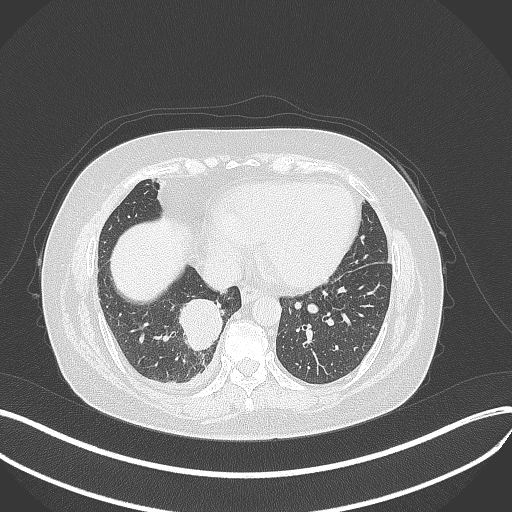
Chest CT, one axial slice. Slice 117 of 381 in the series (ordered by position). 120 kVp. Lung window (W 1500 / L -600 HU). 512 × 512 image matrix, field of view 400 × 400 mm. Patient: female, 56 years. From the clinical record (not read from this slice): clinical TNM (as recorded): T2b N1 M0; histopathological grade: G3.
Annotated regions visible in this slice (bounding box drawn by a radiologist):
- lung tumour (recorded histology: small cell carcinoma): bounding box (x1, y1, x2, y2) in pixels: (176, 294, 223, 354)